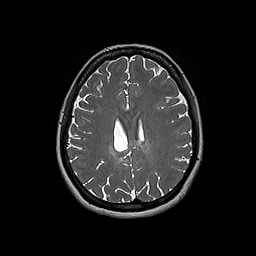
Brain MRI from a brain-tumour surgery series, one axial slice. Position 72 of 192 along the scan axis. 1 mm slice thickness. 256 × 256 image matrix, field of view 250 × 250 mm. From the clinical record (not read from this slice): histopathology: Oligodendroglioma; WHO grade: 2; IDH mutation: yes.
Outlined on this slice (outlined manually by an expert reader):
- tumour: bounding box (x1, y1, x2, y2) in pixels: (109, 146, 123, 162)